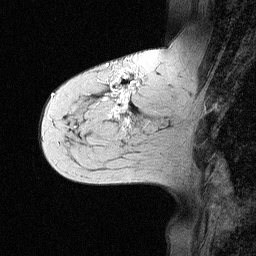
Breast MRI (dynamic contrast-enhanced), one sagittal slice. Position 22 of 64 along the scan axis. Dynamic contrast-enhanced study with each time point stored as its own series, time point 2 of 3 at this slice position (early post-contrast, ordered by acquisition time). 1.5 T. TE 4.5 ms, TR 11 ms. 2.06 mm slice thickness. 256 × 256 image matrix, field of view 200 × 200 mm. Patient: female, 55 years. Case-level facts recorded for this patient, not image findings: setting: breast cancer imaged before/during neoadjuvant chemotherapy; receptor status: triple-negative.
Annotated regions visible in this slice (semi-automatic segmentation, software-assisted and operator-edited):
- analysis volume of interest (the breast-tissue region the enhancement analysis was run in; not a lesion): box from (x=71, y=63) to (x=147, y=145) px
- tumour enhancement mask (voxels above the 90 % enhancement threshold inside the analysis volume of interest): (x=103, y=69)–(x=140, y=125)